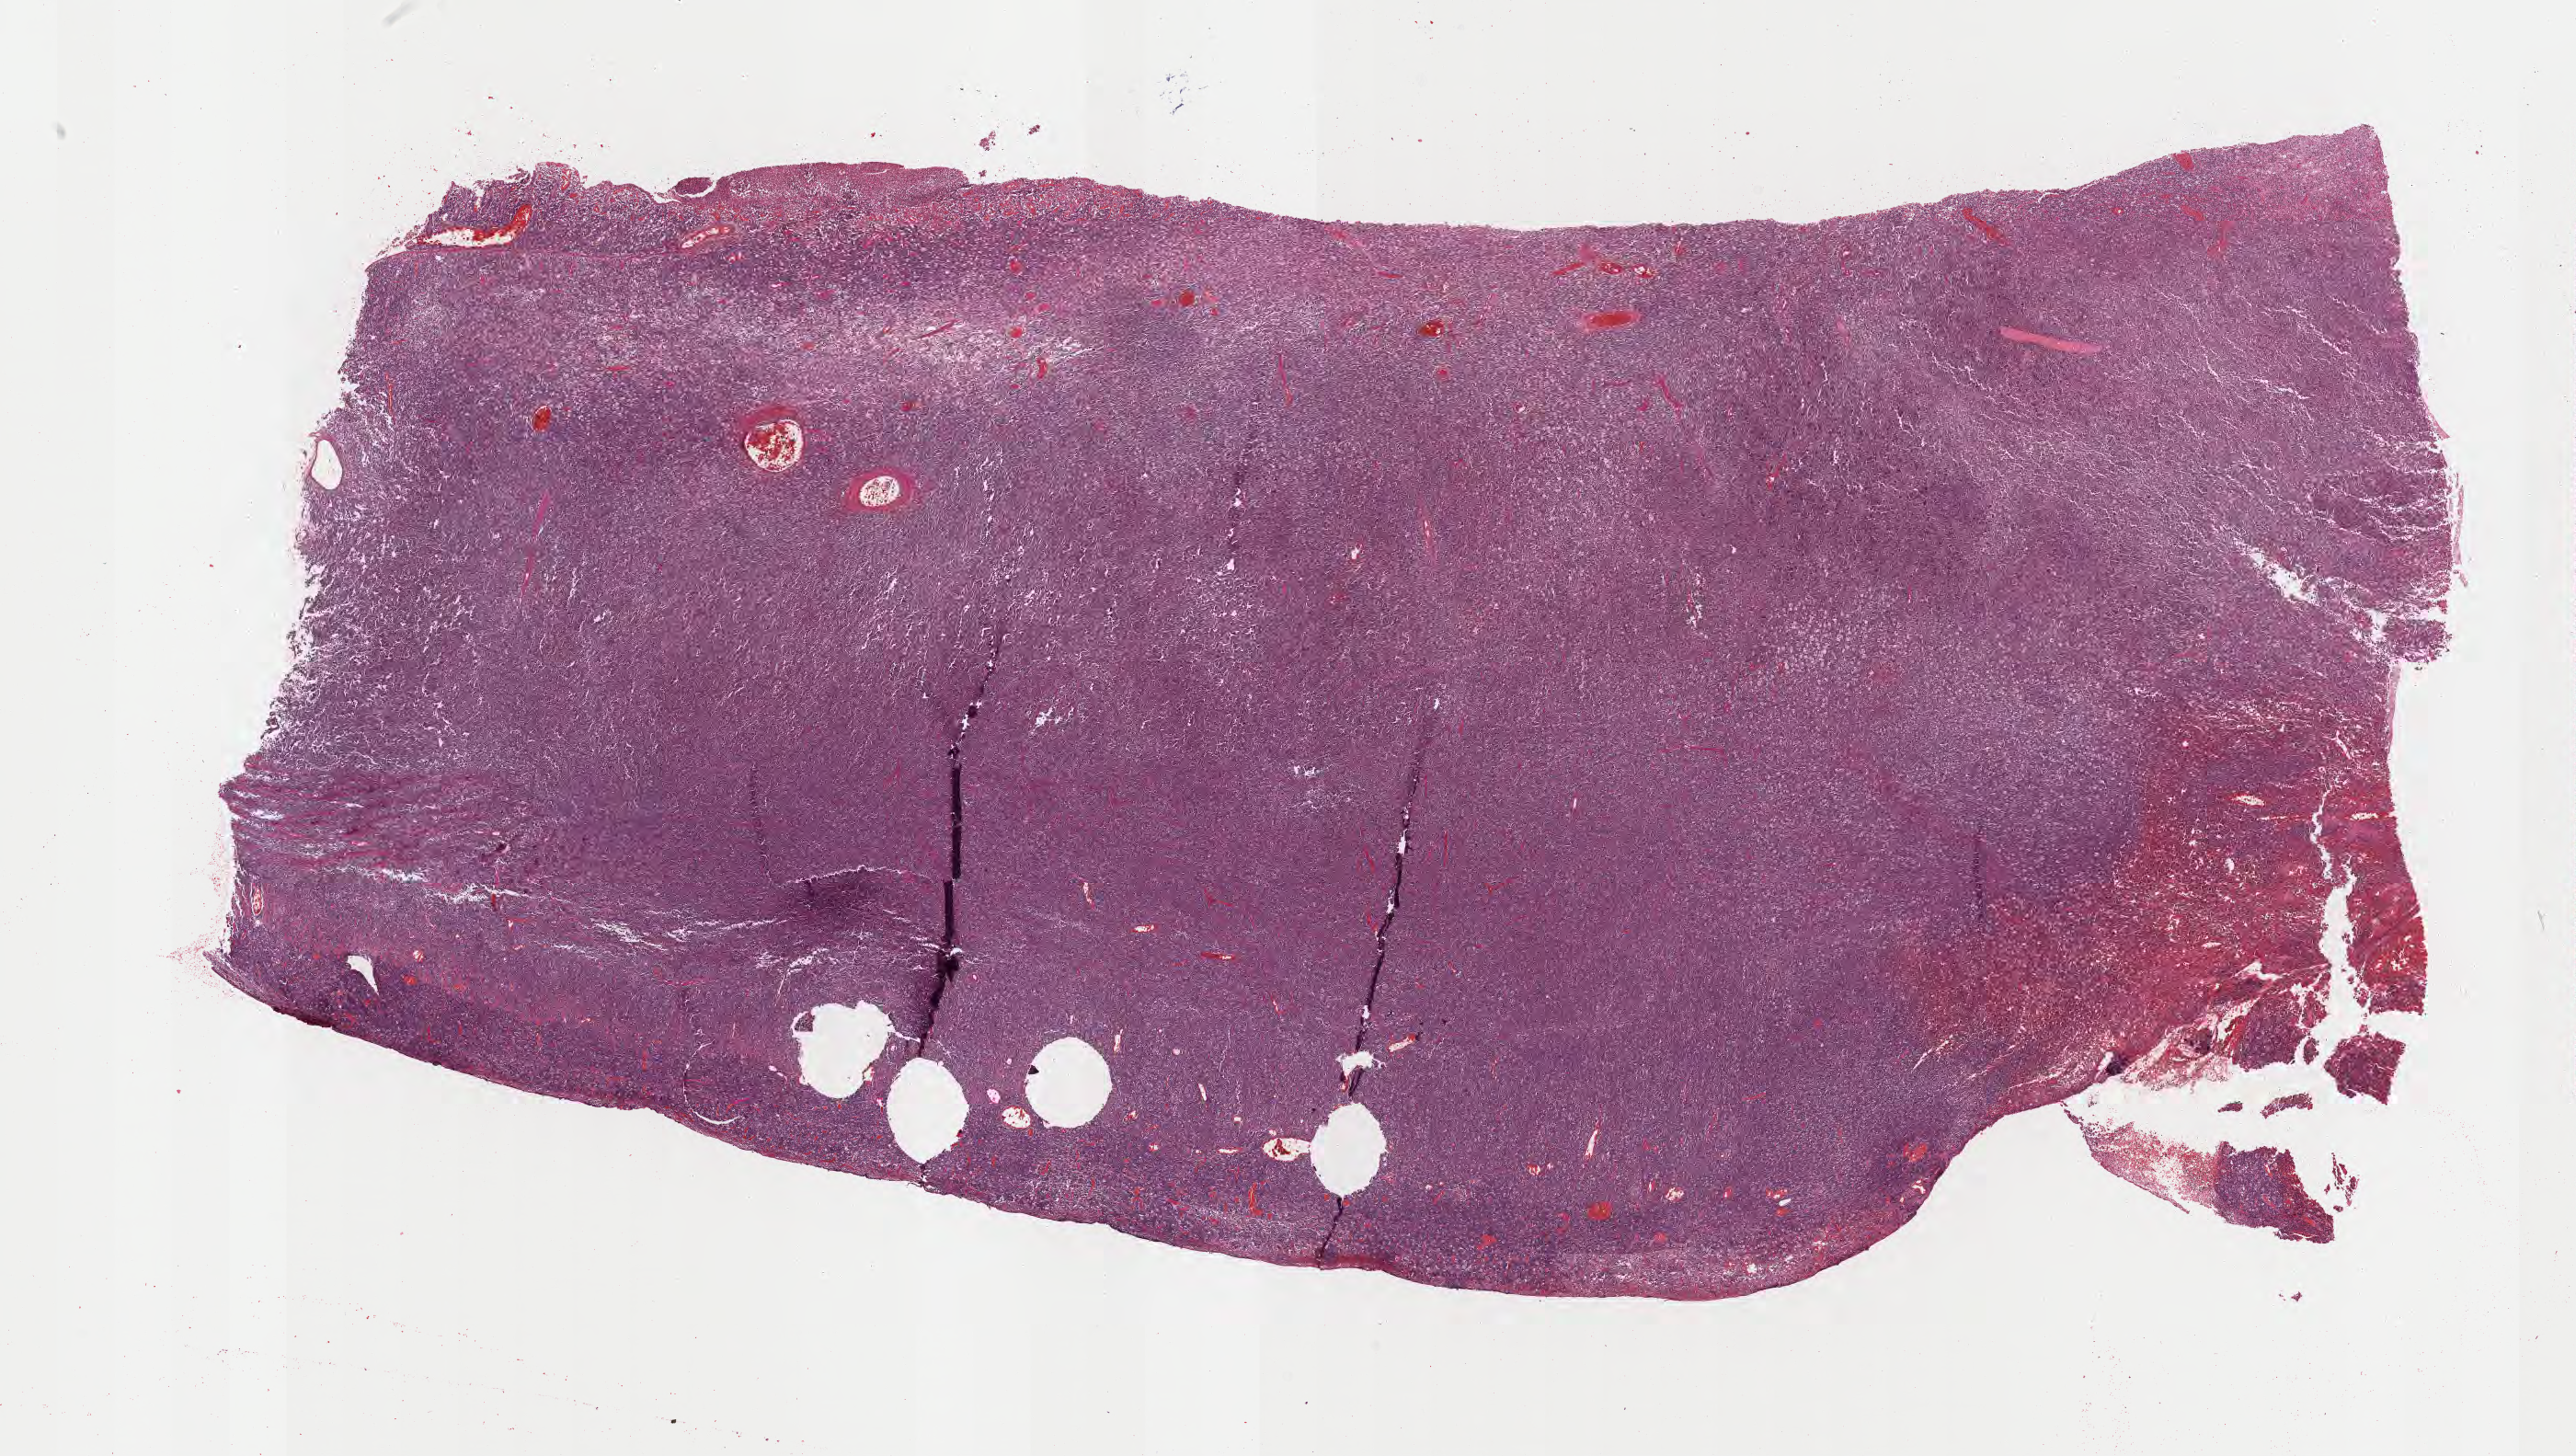
H&E whole-slide image, low-resolution overview of the scanned area, about 22.7 x 12.8 mm; formalin-fixed paraffin-embedded section; primary tumor. Female patient; age at initial diagnosis 6 years. Composition of this section per pathologist review: tumor cells 95%, tumor nuclei 95%, stromal cells 5%, necrosis 0%, normal cells 0%. Infiltration values recorded for this section: lymphocyte infiltration 50%, monocyte infiltration 20%, neutrophil infiltration 5%.
Section: top of the tissue portion. Histologic diagnosis: Burkitt lymphoma, NOS. Ann Arbor stage (patient): Stage IV.